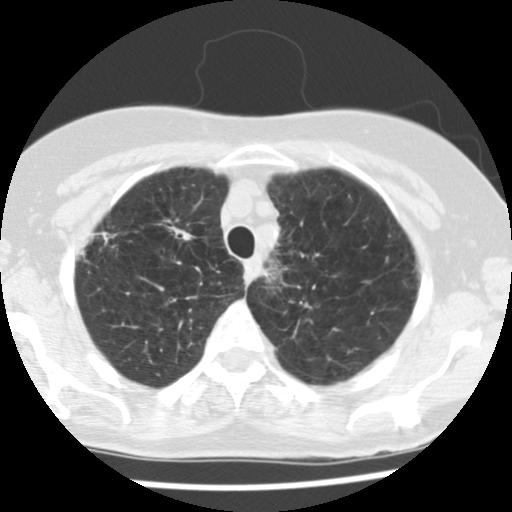
Axial slice from a low-dose chest CT screening exam. Baseline annual screen. Lung window (W 1500 / L -600 HU). 2.5 mm slice thickness. Slice 24 of 121 in the series. Female participant, aged 70 years at enrolment.
• Lesion marked by an expert reader, box from (x=152, y=206) to (x=212, y=256) px.
• Reader record for this screening exam (exam-level; its link to the box is not recorded): non-calcified nodule or mass ≥4 mm, left upper lobe, 8 × 6 mm, poorly defined margins, soft tissue attenuation.
• Note: the box lies in the patient's right hemithorax on this image, whereas the reader's record names the left lung; they may be different findings.
• Participant outcome: lung cancer diagnosed 745 days after this screen (after the second annual screen) — non-small cell carcinoma, right upper lobe, stage IV (AJCC 6th edition), 30 mm at pathology.